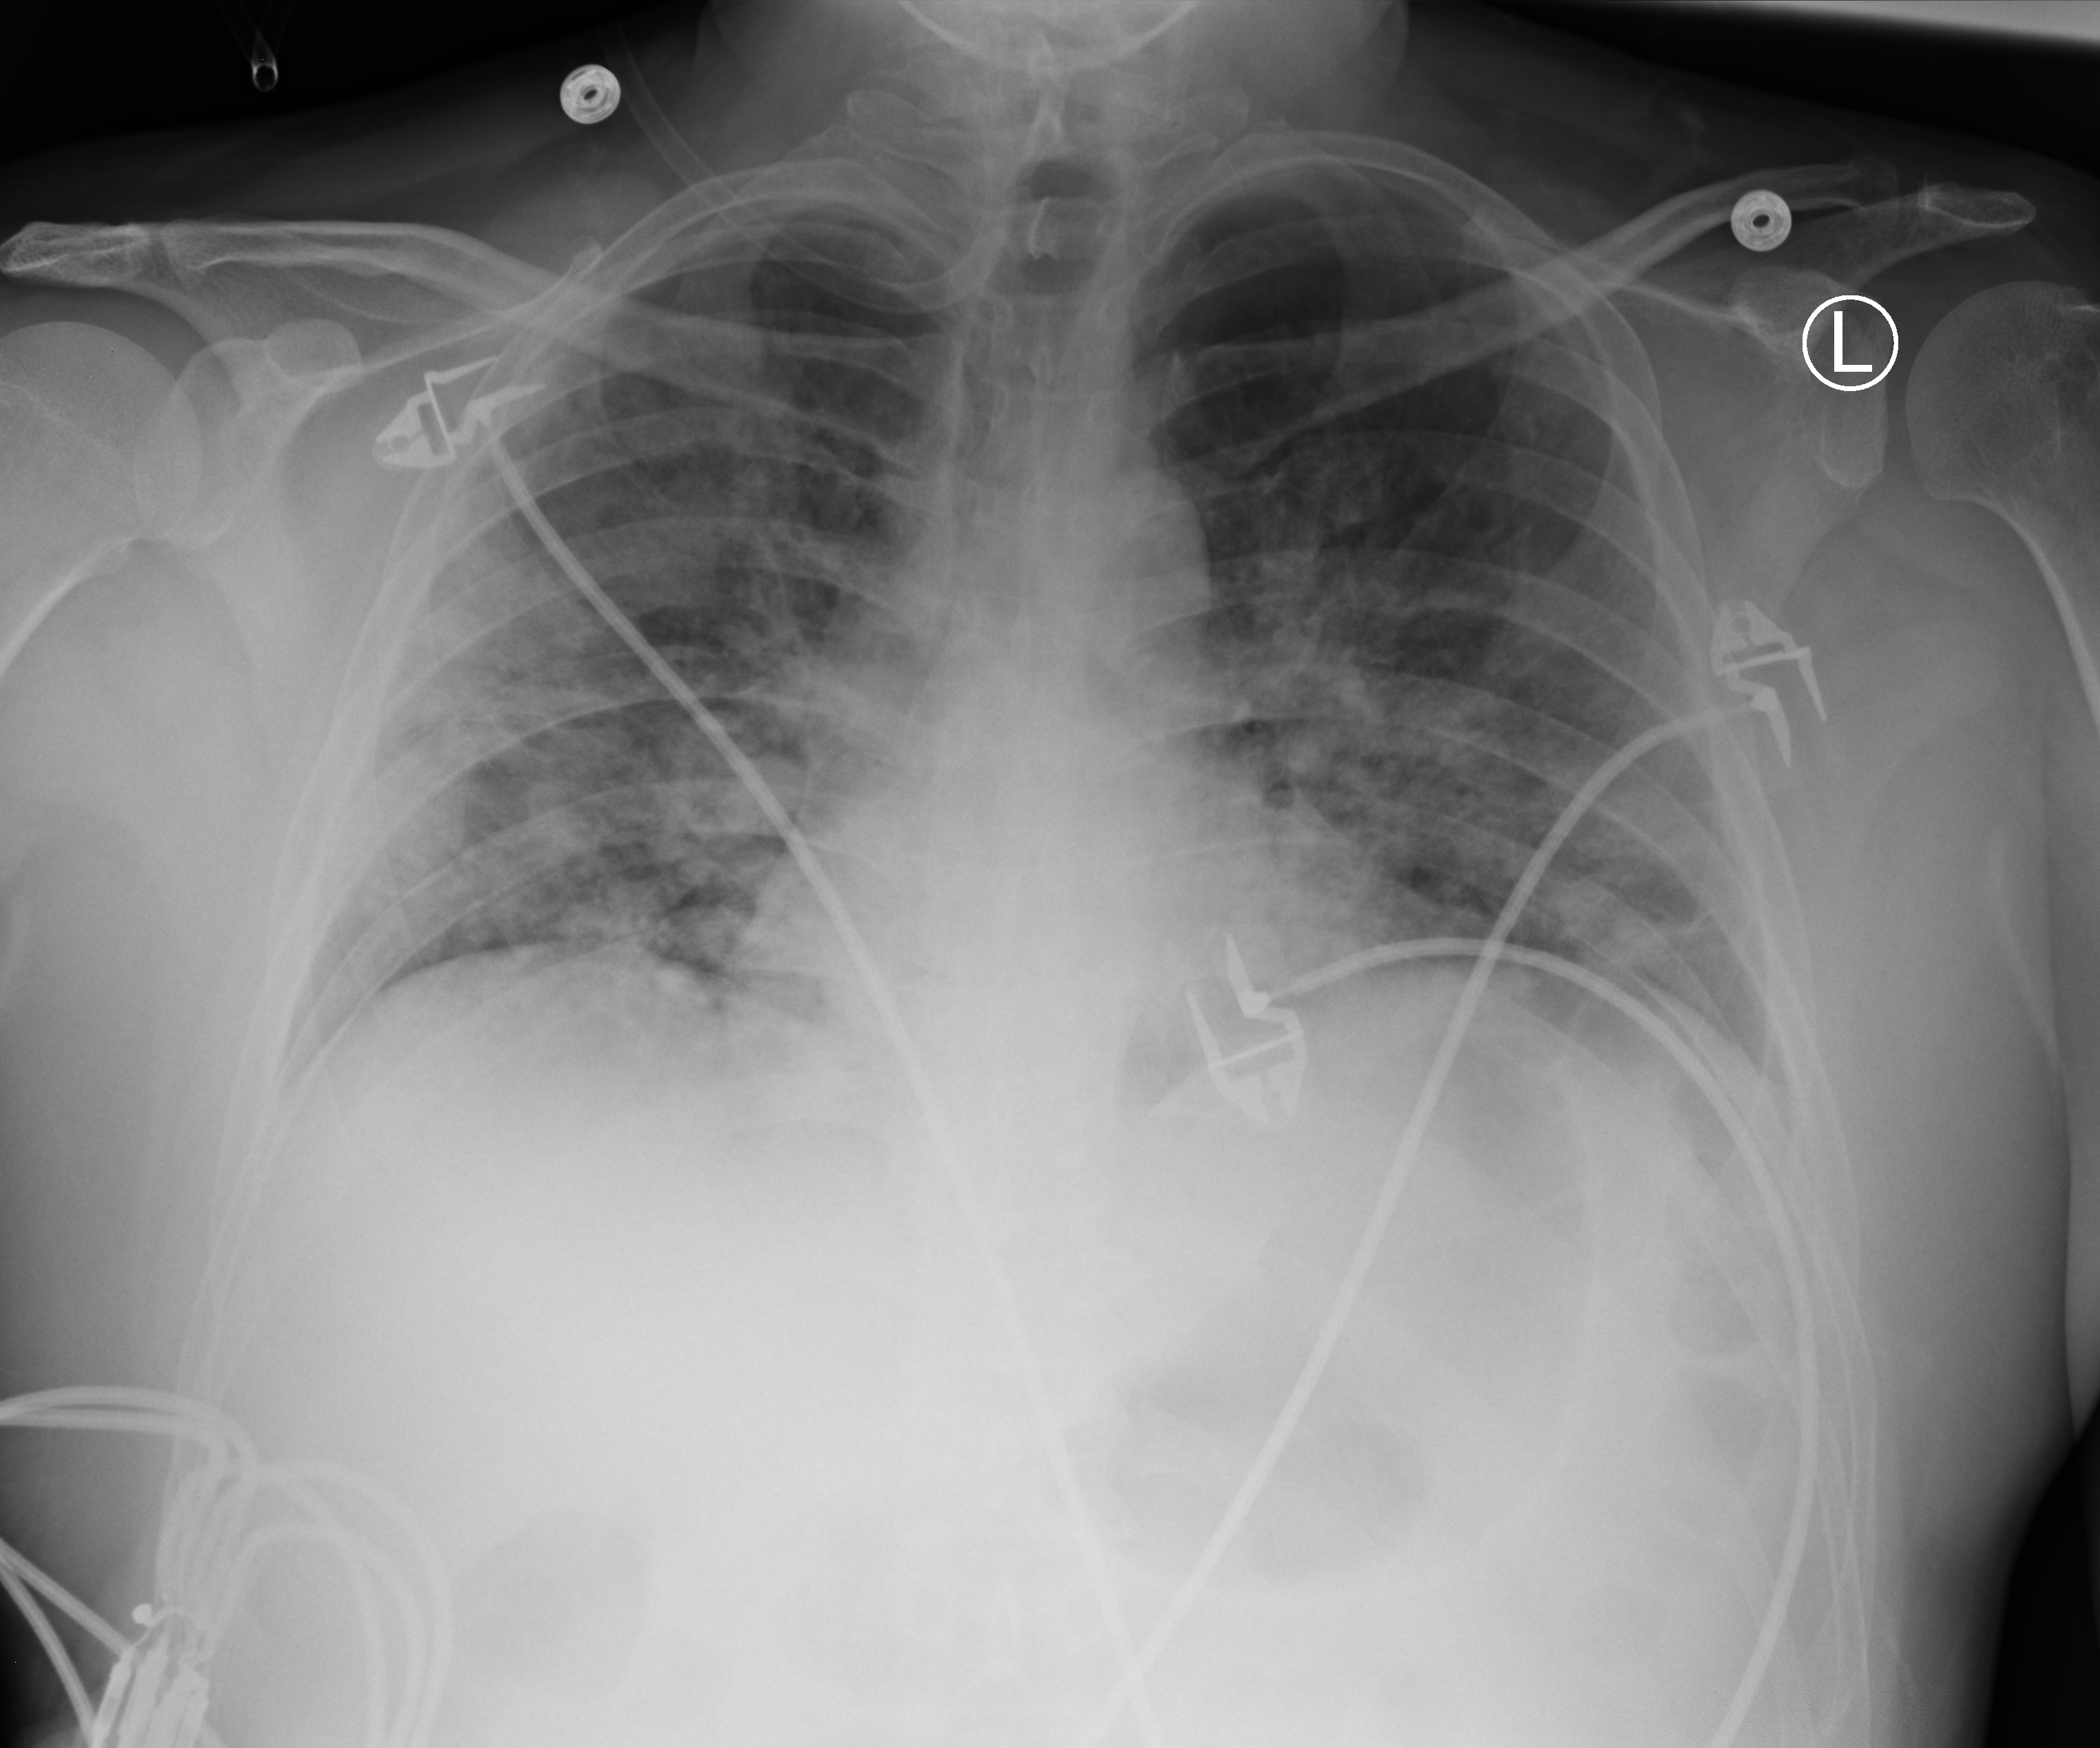
Portable chest radiograph; anteroposterior (AP) projection. Patient hospitalised with COVID-19; male, aged 18–59 years.
Hospital-stay facts (about this admission, not read from this image; timing relative to this image not recorded):
- mechanically ventilated during this hospital stay: no
- other chronic lung disease (admission record): no
- length of hospital stay: 10 days